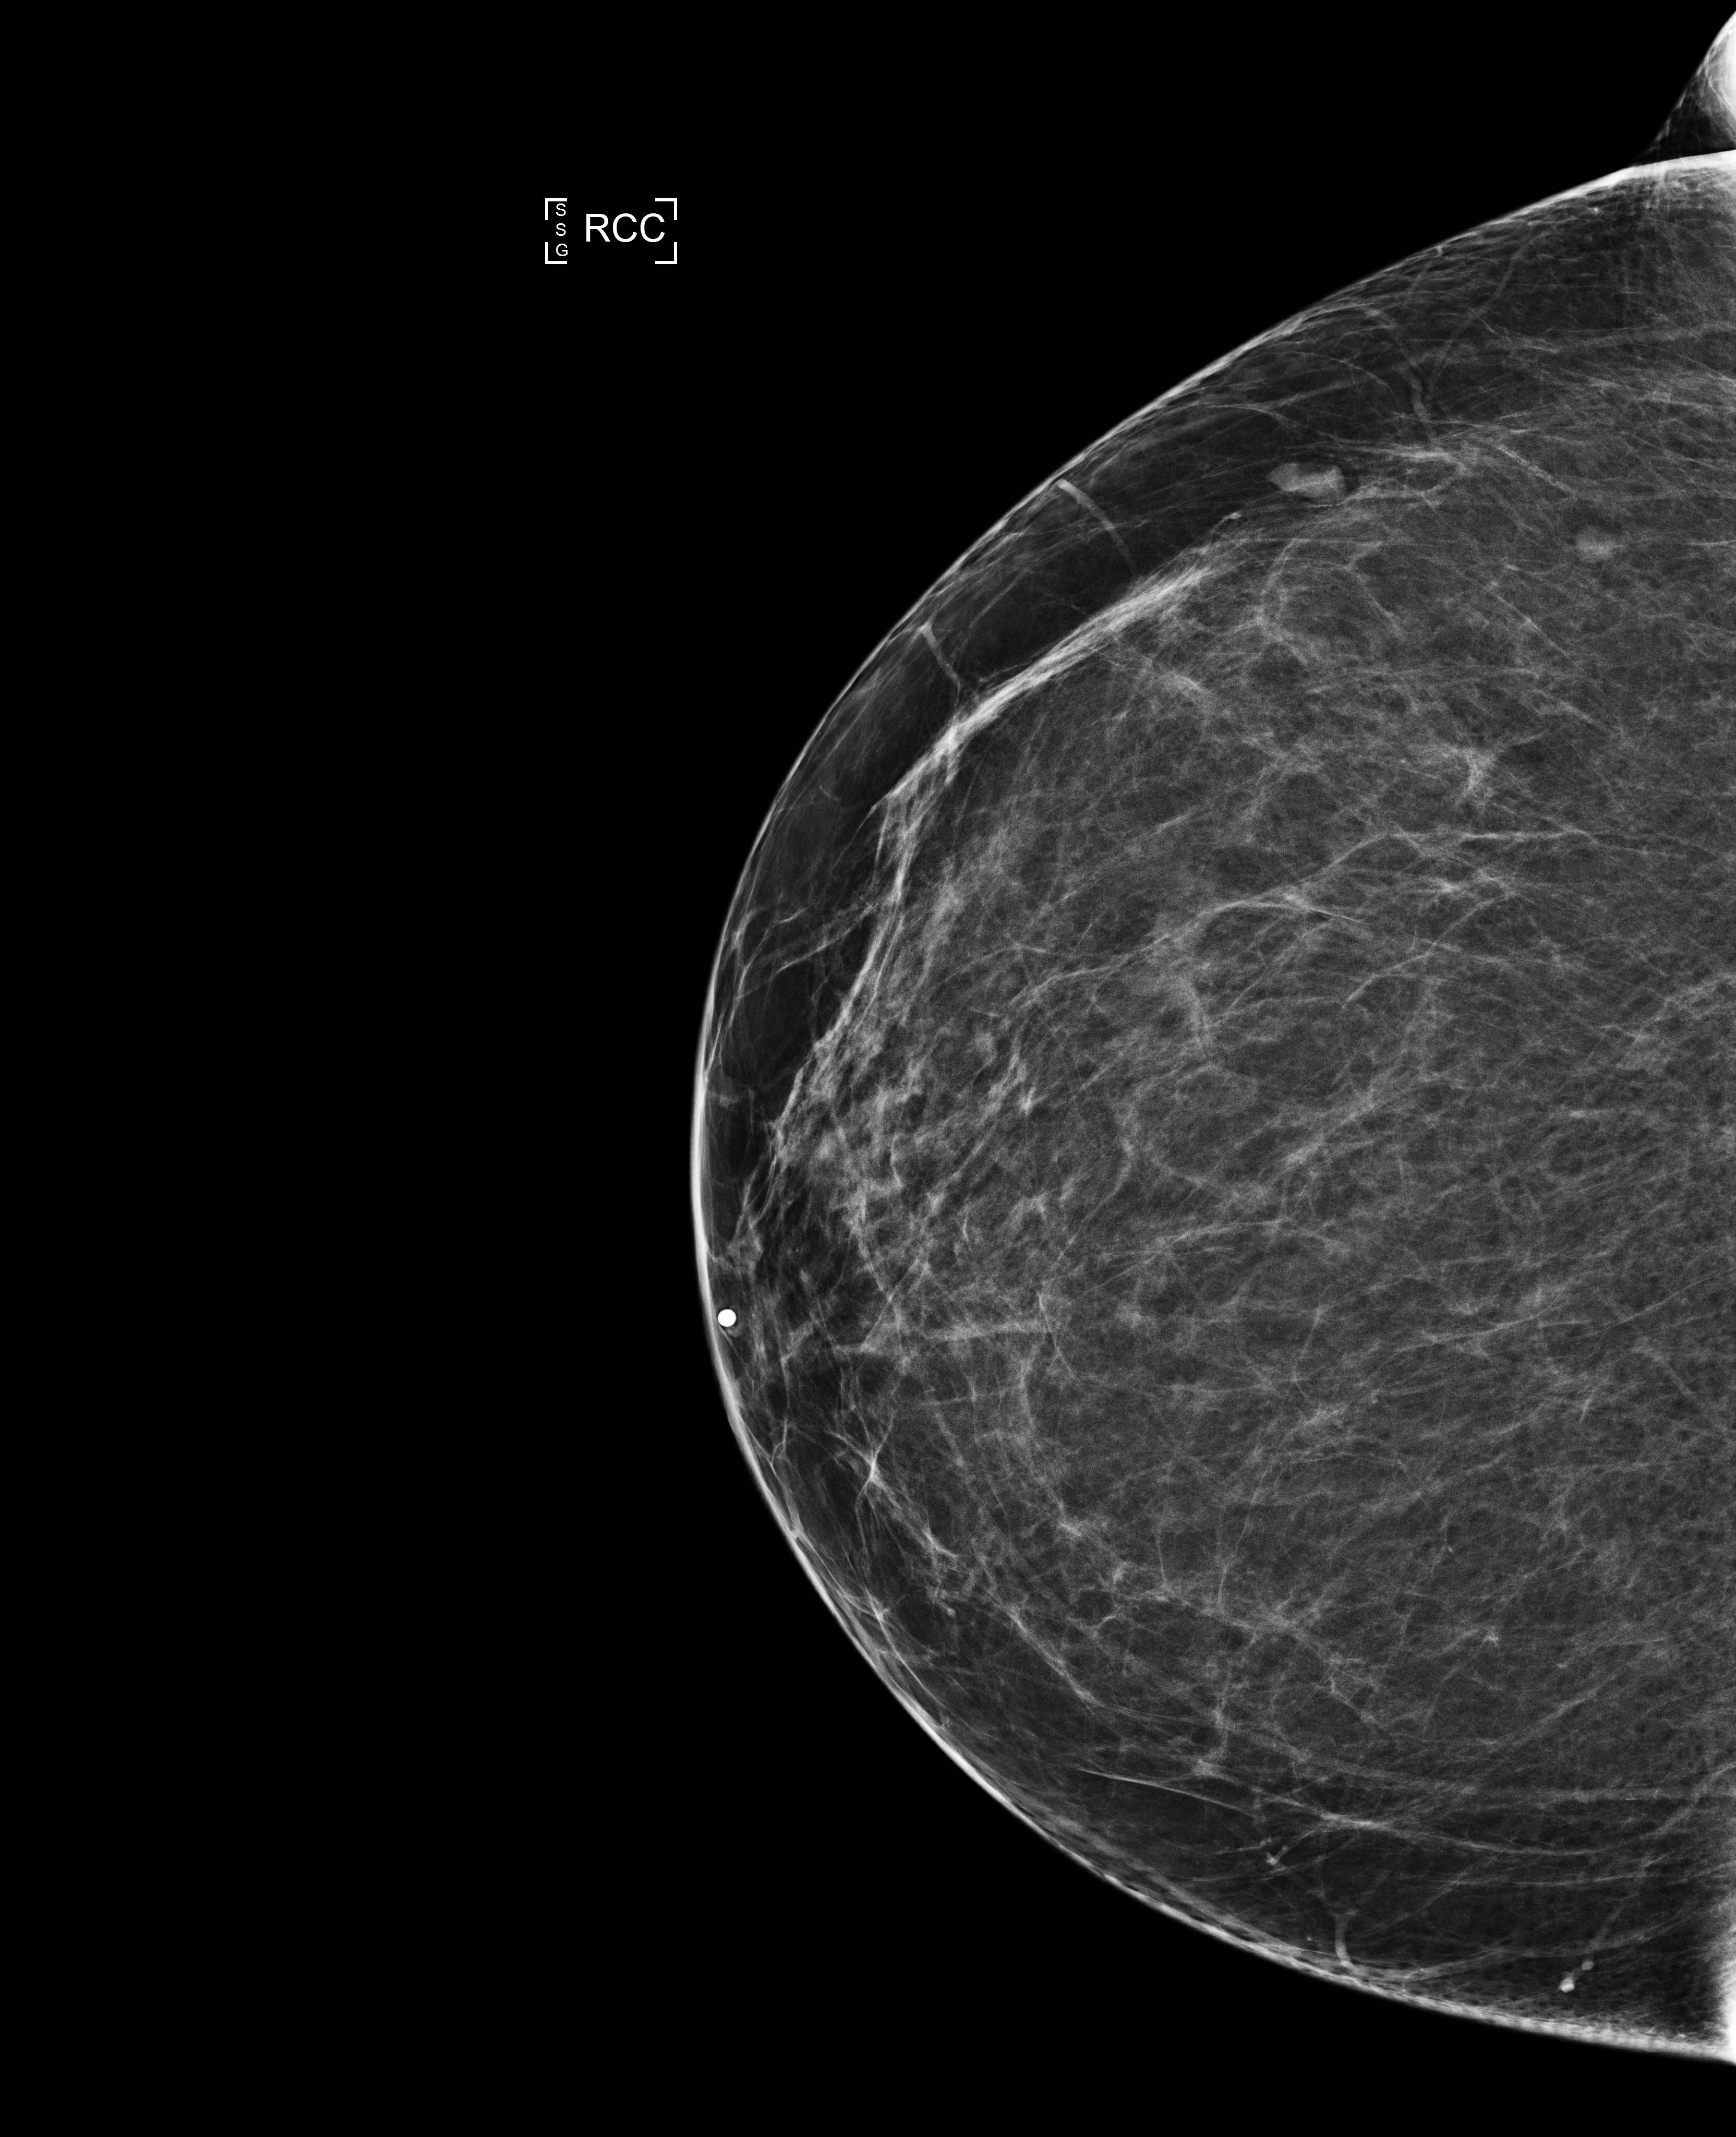
Full-field digital mammogram (FFDM); right breast; cranio-caudal projection; annual screening mammography examination; system: Selenia Dimensions. Female patient, age 51 years.
Breast density at the screening exam (both breasts): scattered fibroglandular densities (BI-RADS density category b).